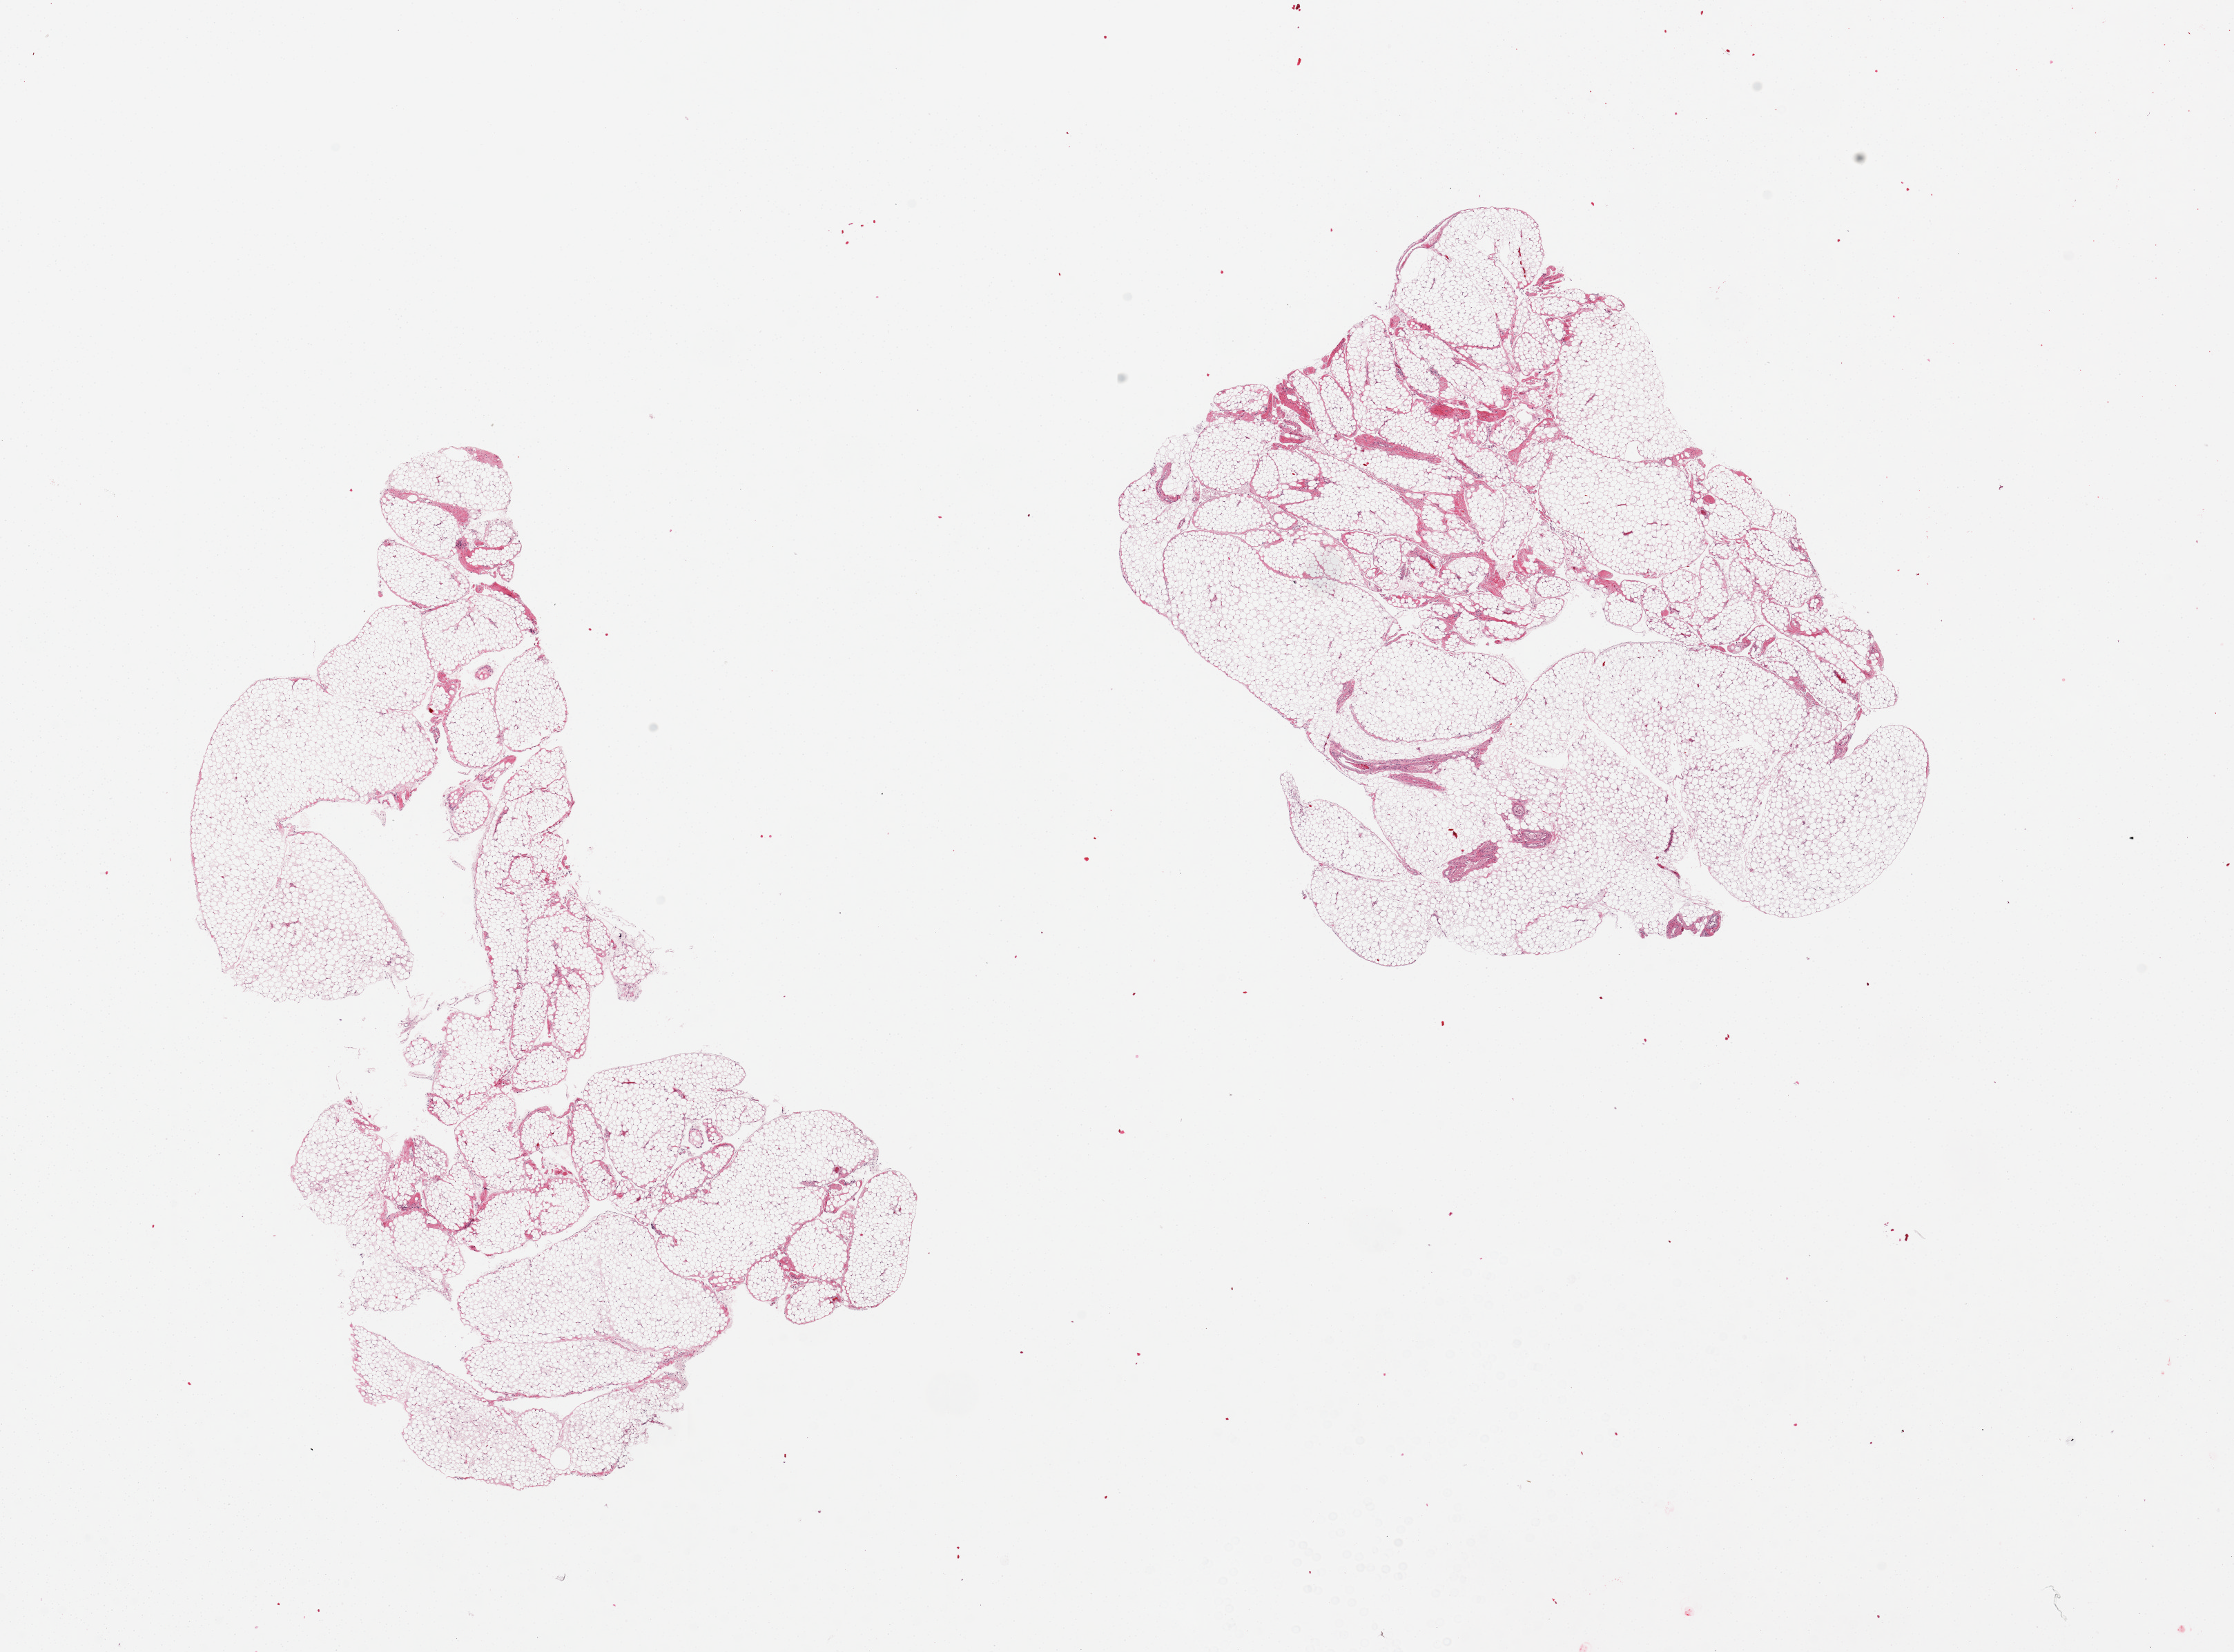
Haematoxylin and eosin whole-slide image, brightfield — shown as a low-resolution overview of the whole scanned area (about 25.6 x 18.9 mm); PAXgene-fixed paraffin-embedded (PFPE) section; section of omentum (target tissue); donor tissue sample. Female donor.
Review note (as recorded): 2 pieces, one is ~10% fibrous tissue.